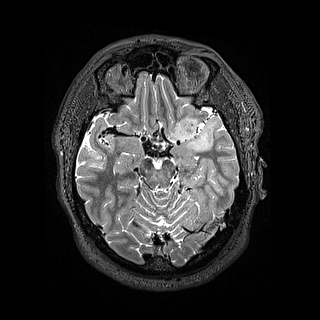
Brain MRI from a brain-tumour surgery series, one axial slice. Position 99 of 144 along the scan axis. 1.2 mm slice thickness. 320 × 320 image matrix, field of view 254 × 254 mm. From the clinical record (not read from this slice): histopathology: Astrocytoma; WHO grade: 2; IDH mutation: yes.
Annotated regions visible in this slice (outlined manually by an expert reader):
- tumour: bounding box [x1, y1, x2, y2] px = [172, 113, 205, 153]